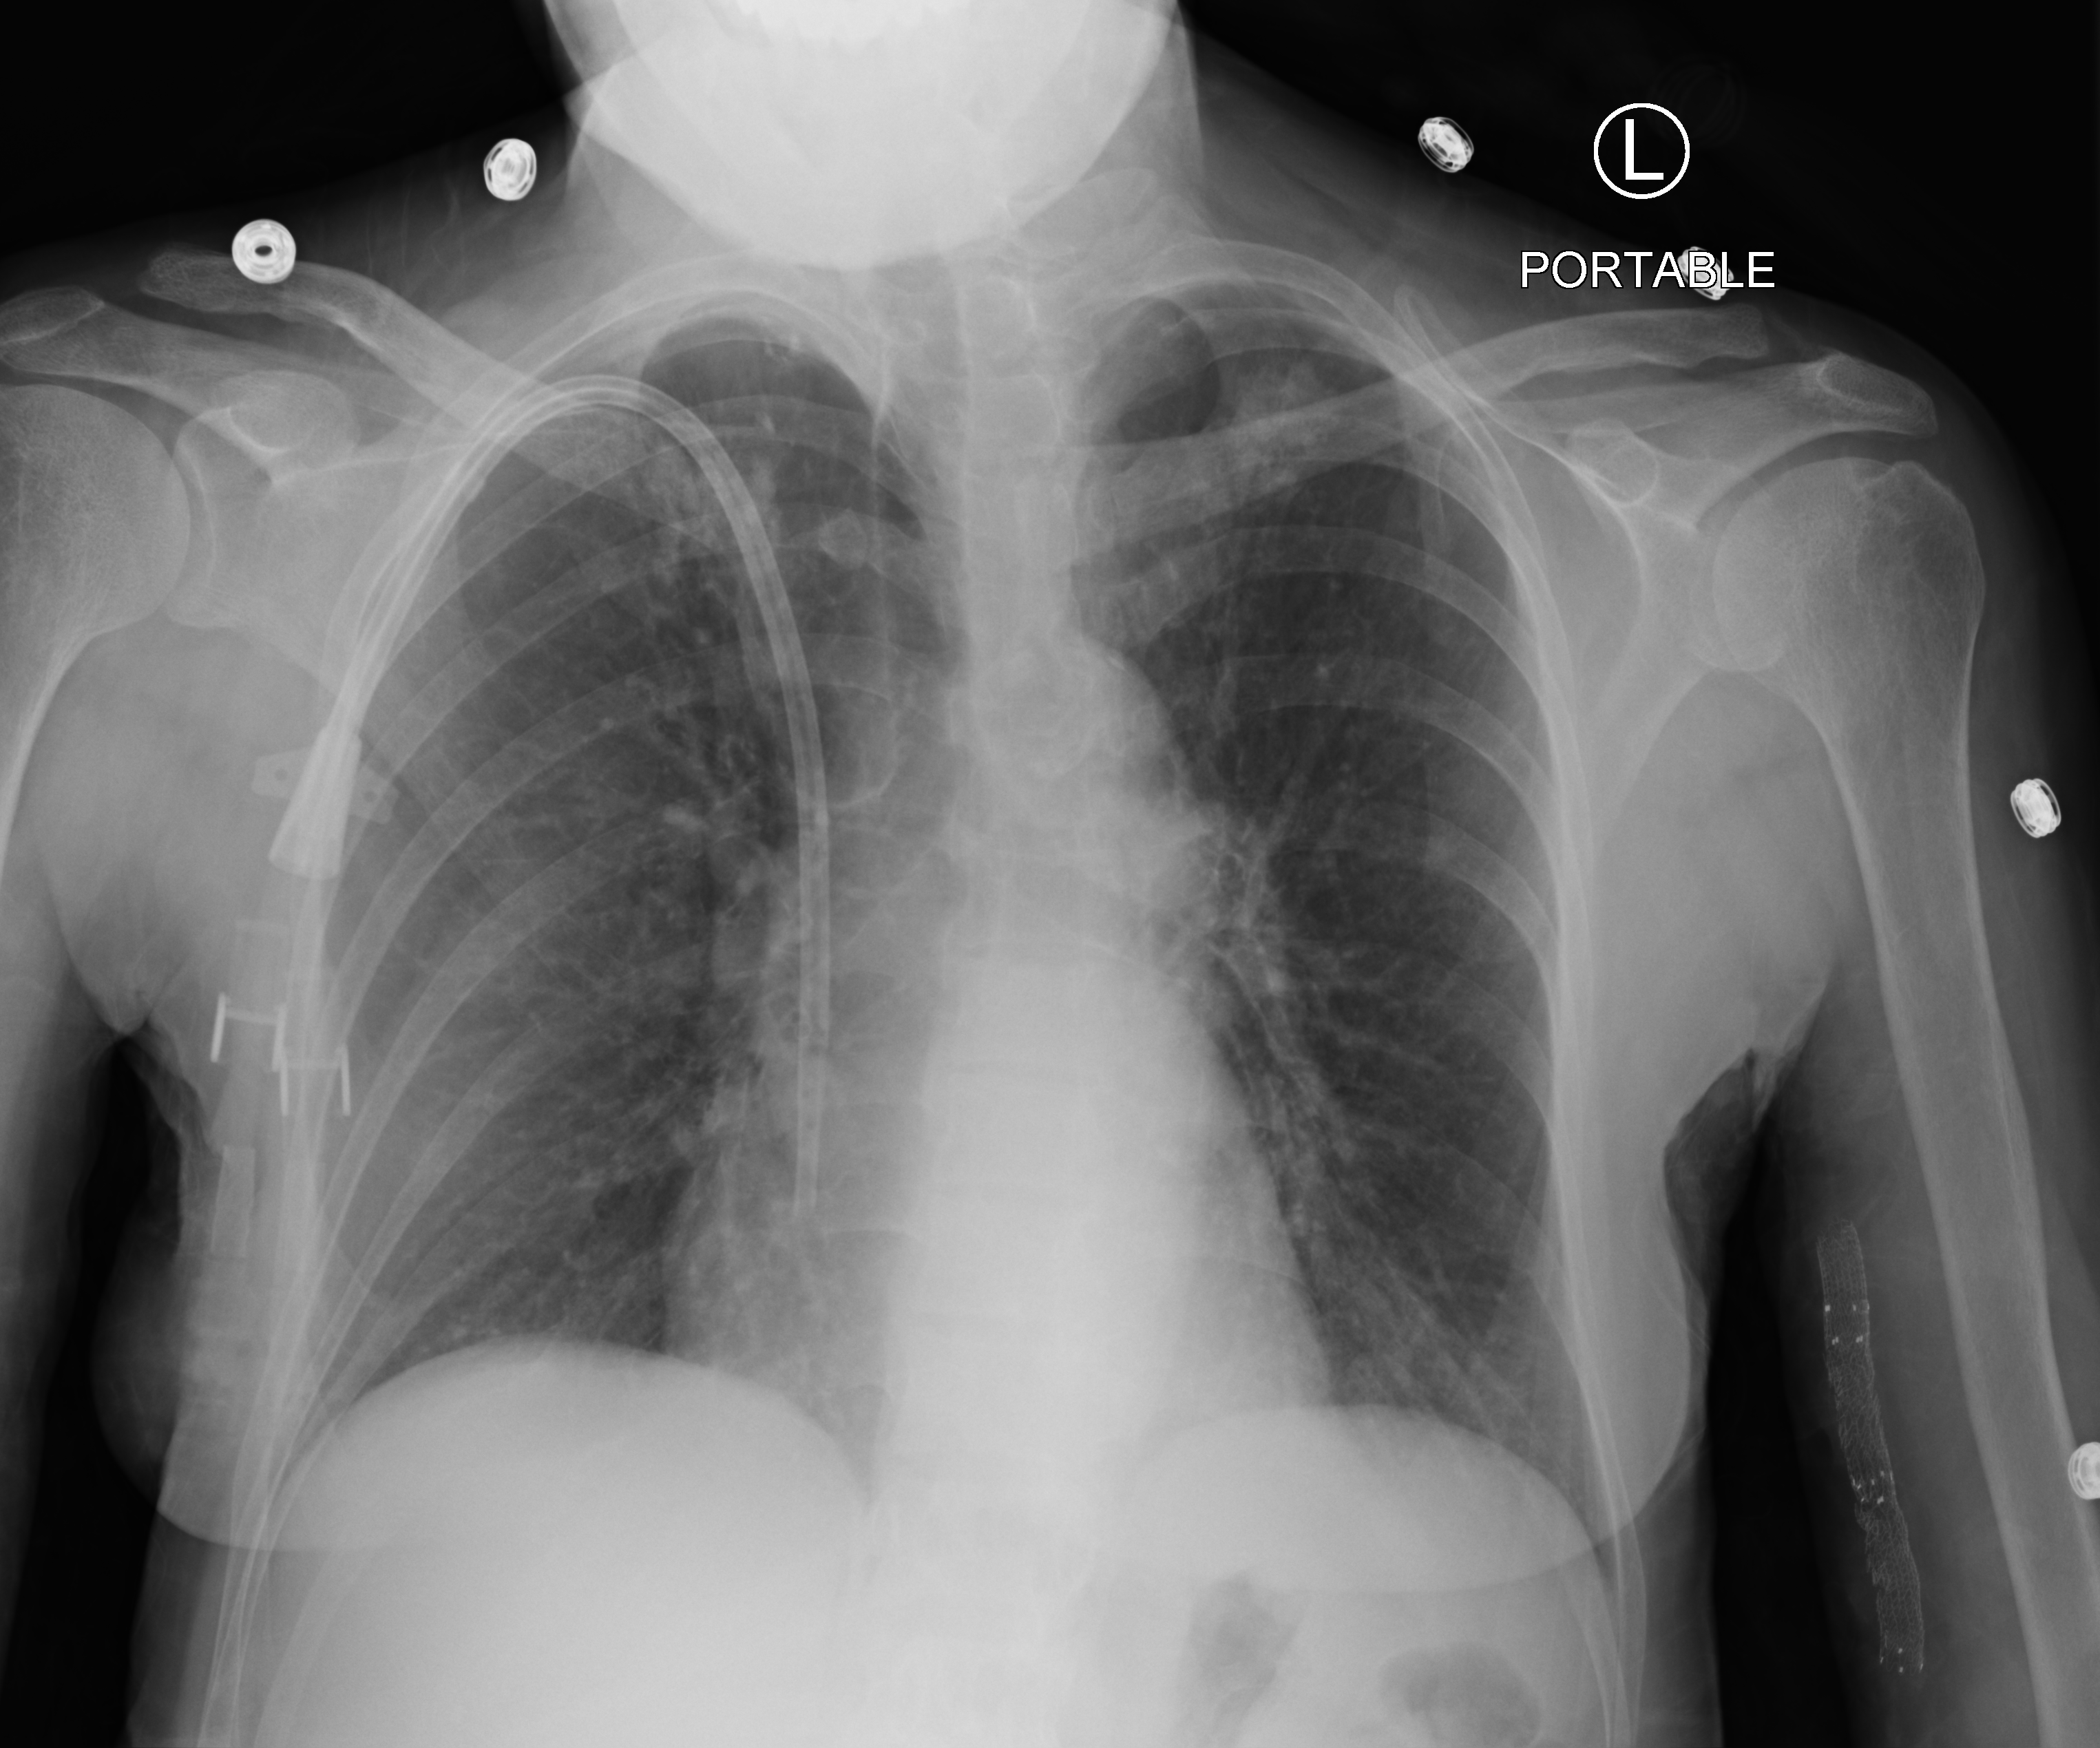
Portable chest radiograph. Patient hospitalised with COVID-19; female, aged 18–59 years.
Admission-level facts for this patient (not findings on this image; timing relative to this image not recorded):
- admitted to intensive care during this hospital stay: no
- mechanically ventilated during this hospital stay: no